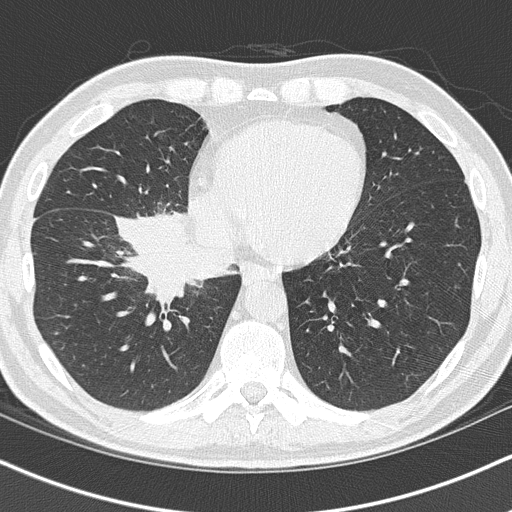
Axial slice from a low-dose chest CT screening exam; first (baseline) screen; lung window (W 1500 / L -600 HU); 2 mm slice thickness; 120 kVp; slice 42 of 151 in the series. Male participant, aged 55 years at enrolment. Current smoker at enrolment.
Lesion marked by an expert reader, bounding box [x1, y1, x2, y2] px = [122, 223, 243, 315]. The exam's reader record, not a measurement of the box and not confirmed to be the same lesion: non-calcified nodule or mass ≥4 mm, right lower lobe, 6 × 5 mm, spiculated (stellate) margins, soft tissue attenuation. Official screen result: positive, change unspecified: nodule(s) >= 4 mm or enlarging nodule(s), mass(es), or other non-specific abnormalities suspicious for lung cancer. Participant outcome: lung cancer diagnosed 21 days after this screen — carcinoma, NOS, right hilum, stage IB (AJCC 6th edition), 67 mm at pathology.